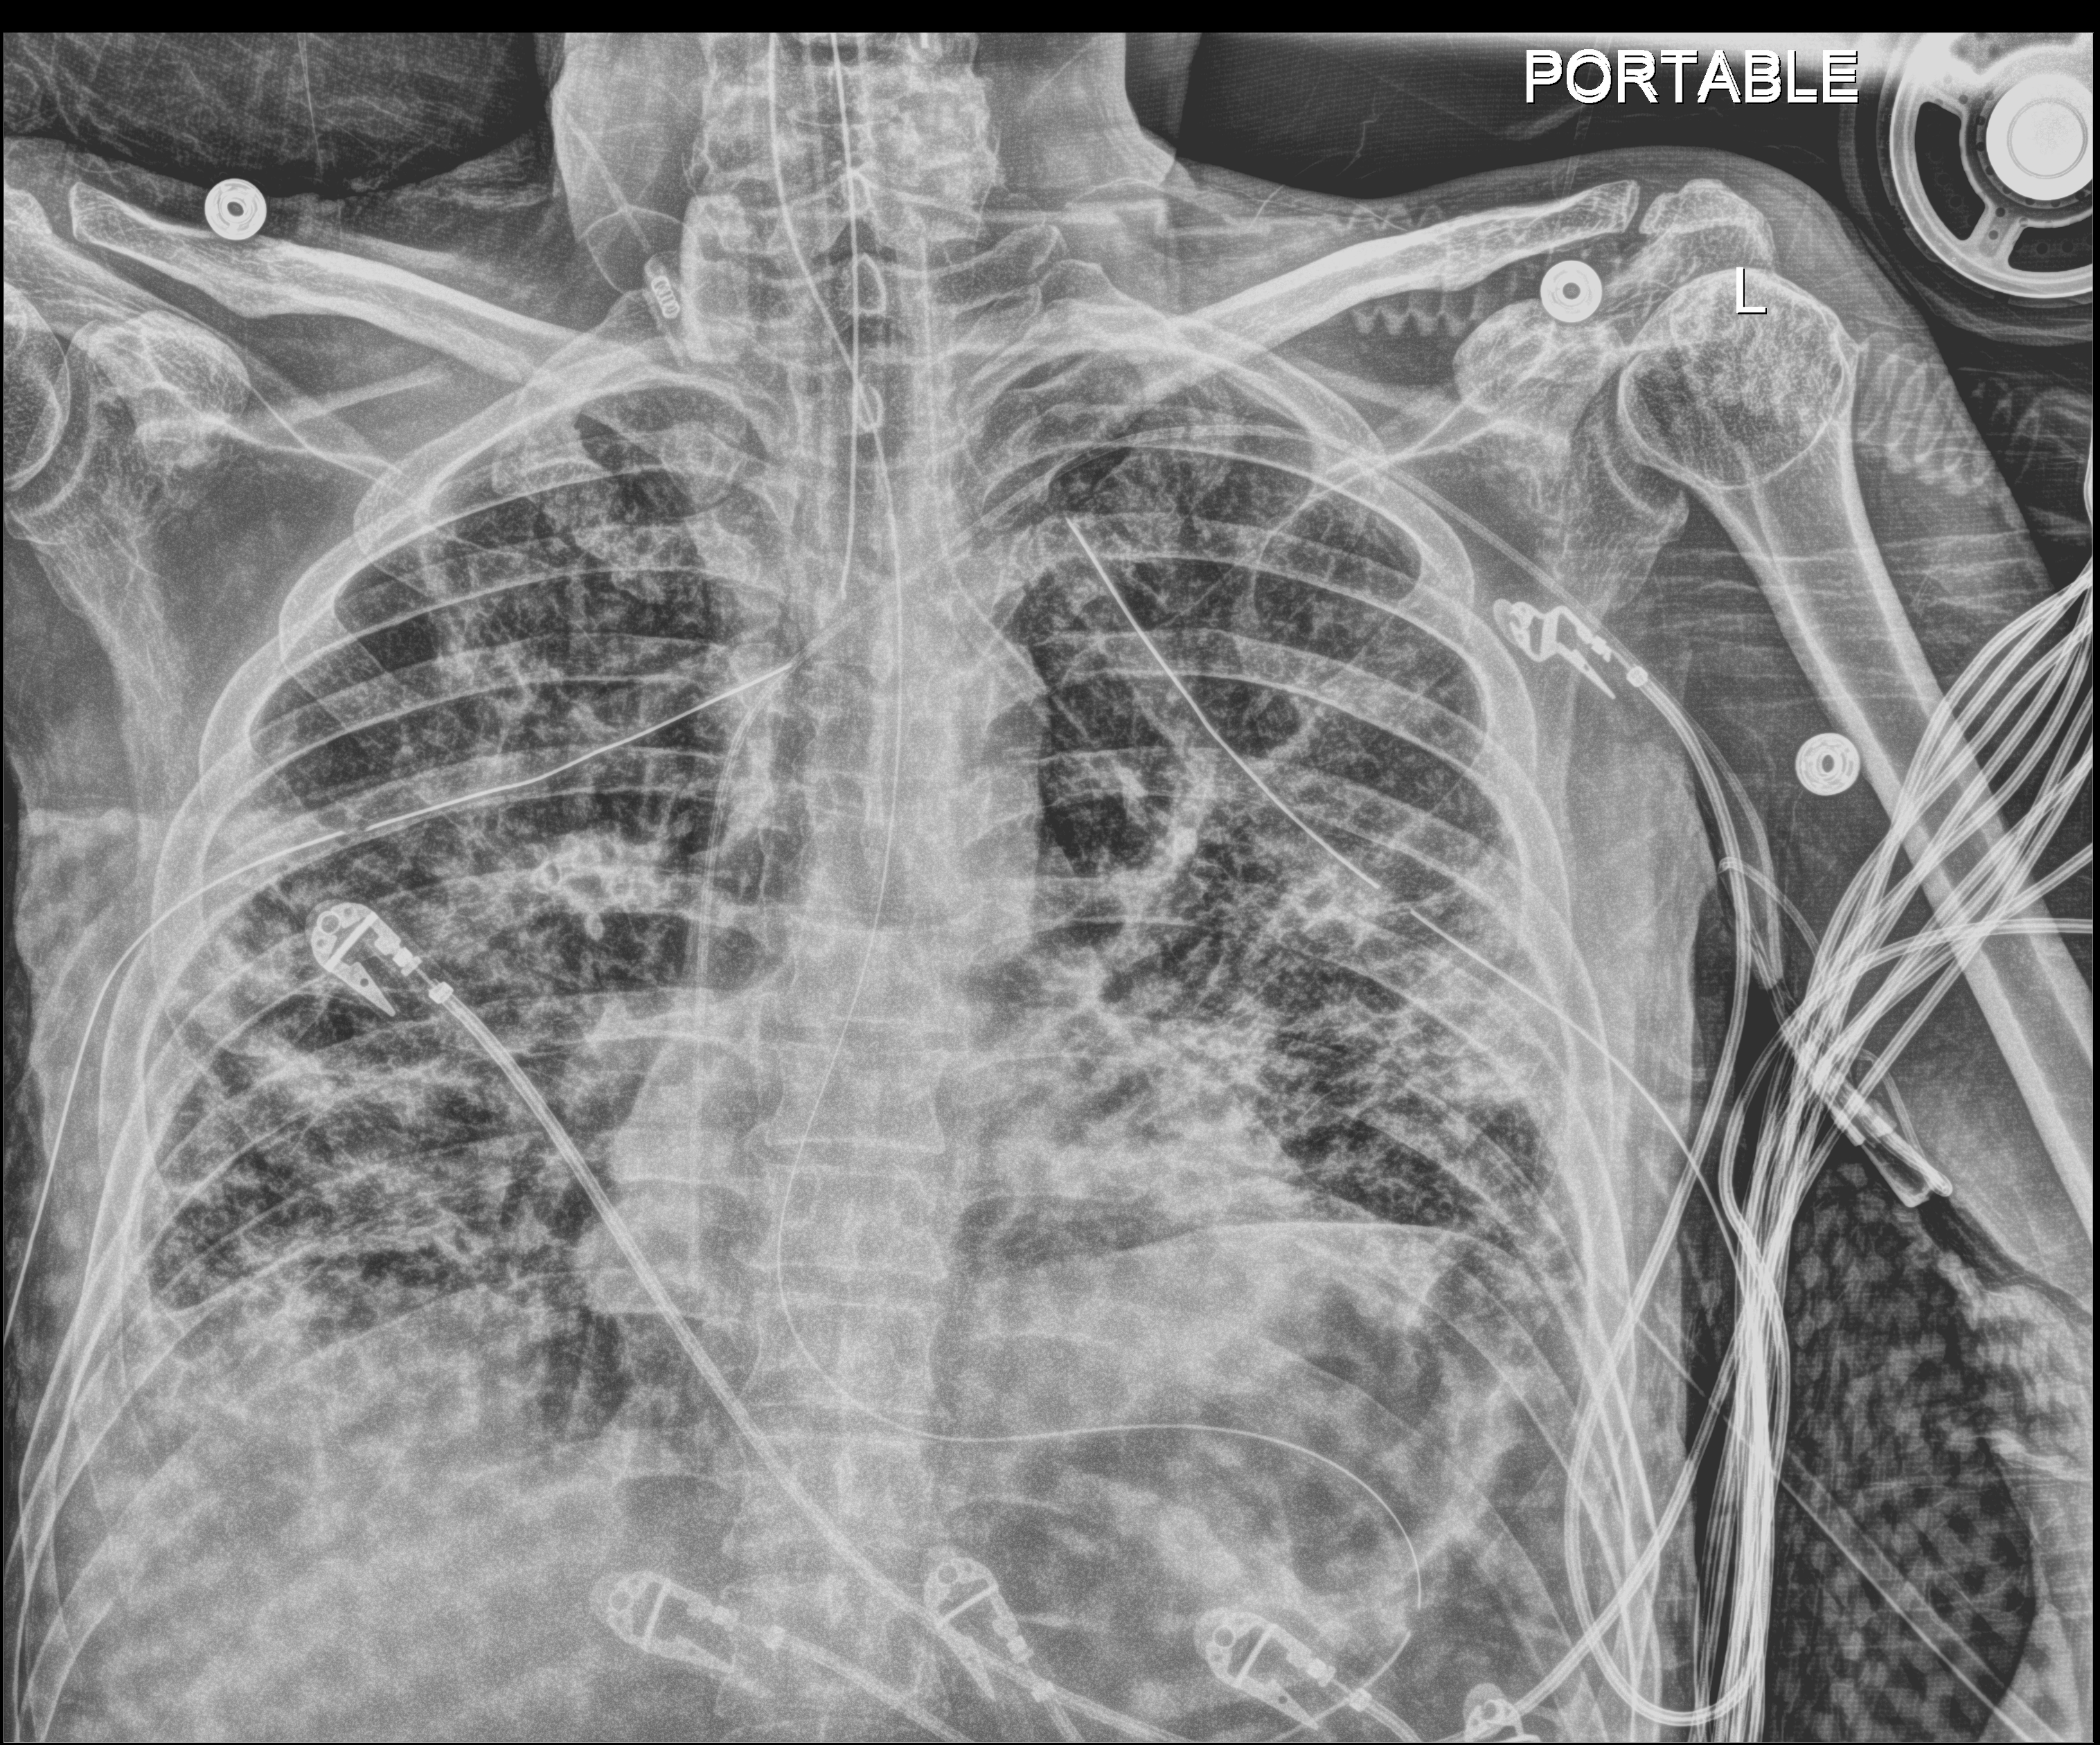
Chest X-ray (portable); anteroposterior (AP) projection. Patient hospitalised with COVID-19; male, aged 18–59 years.
Hospital-stay facts (about this admission, not read from this image; timing relative to this image not recorded): mechanically ventilated during this hospital stay: yes; diabetes (admission record): yes; admitted to intensive care during this hospital stay: yes.